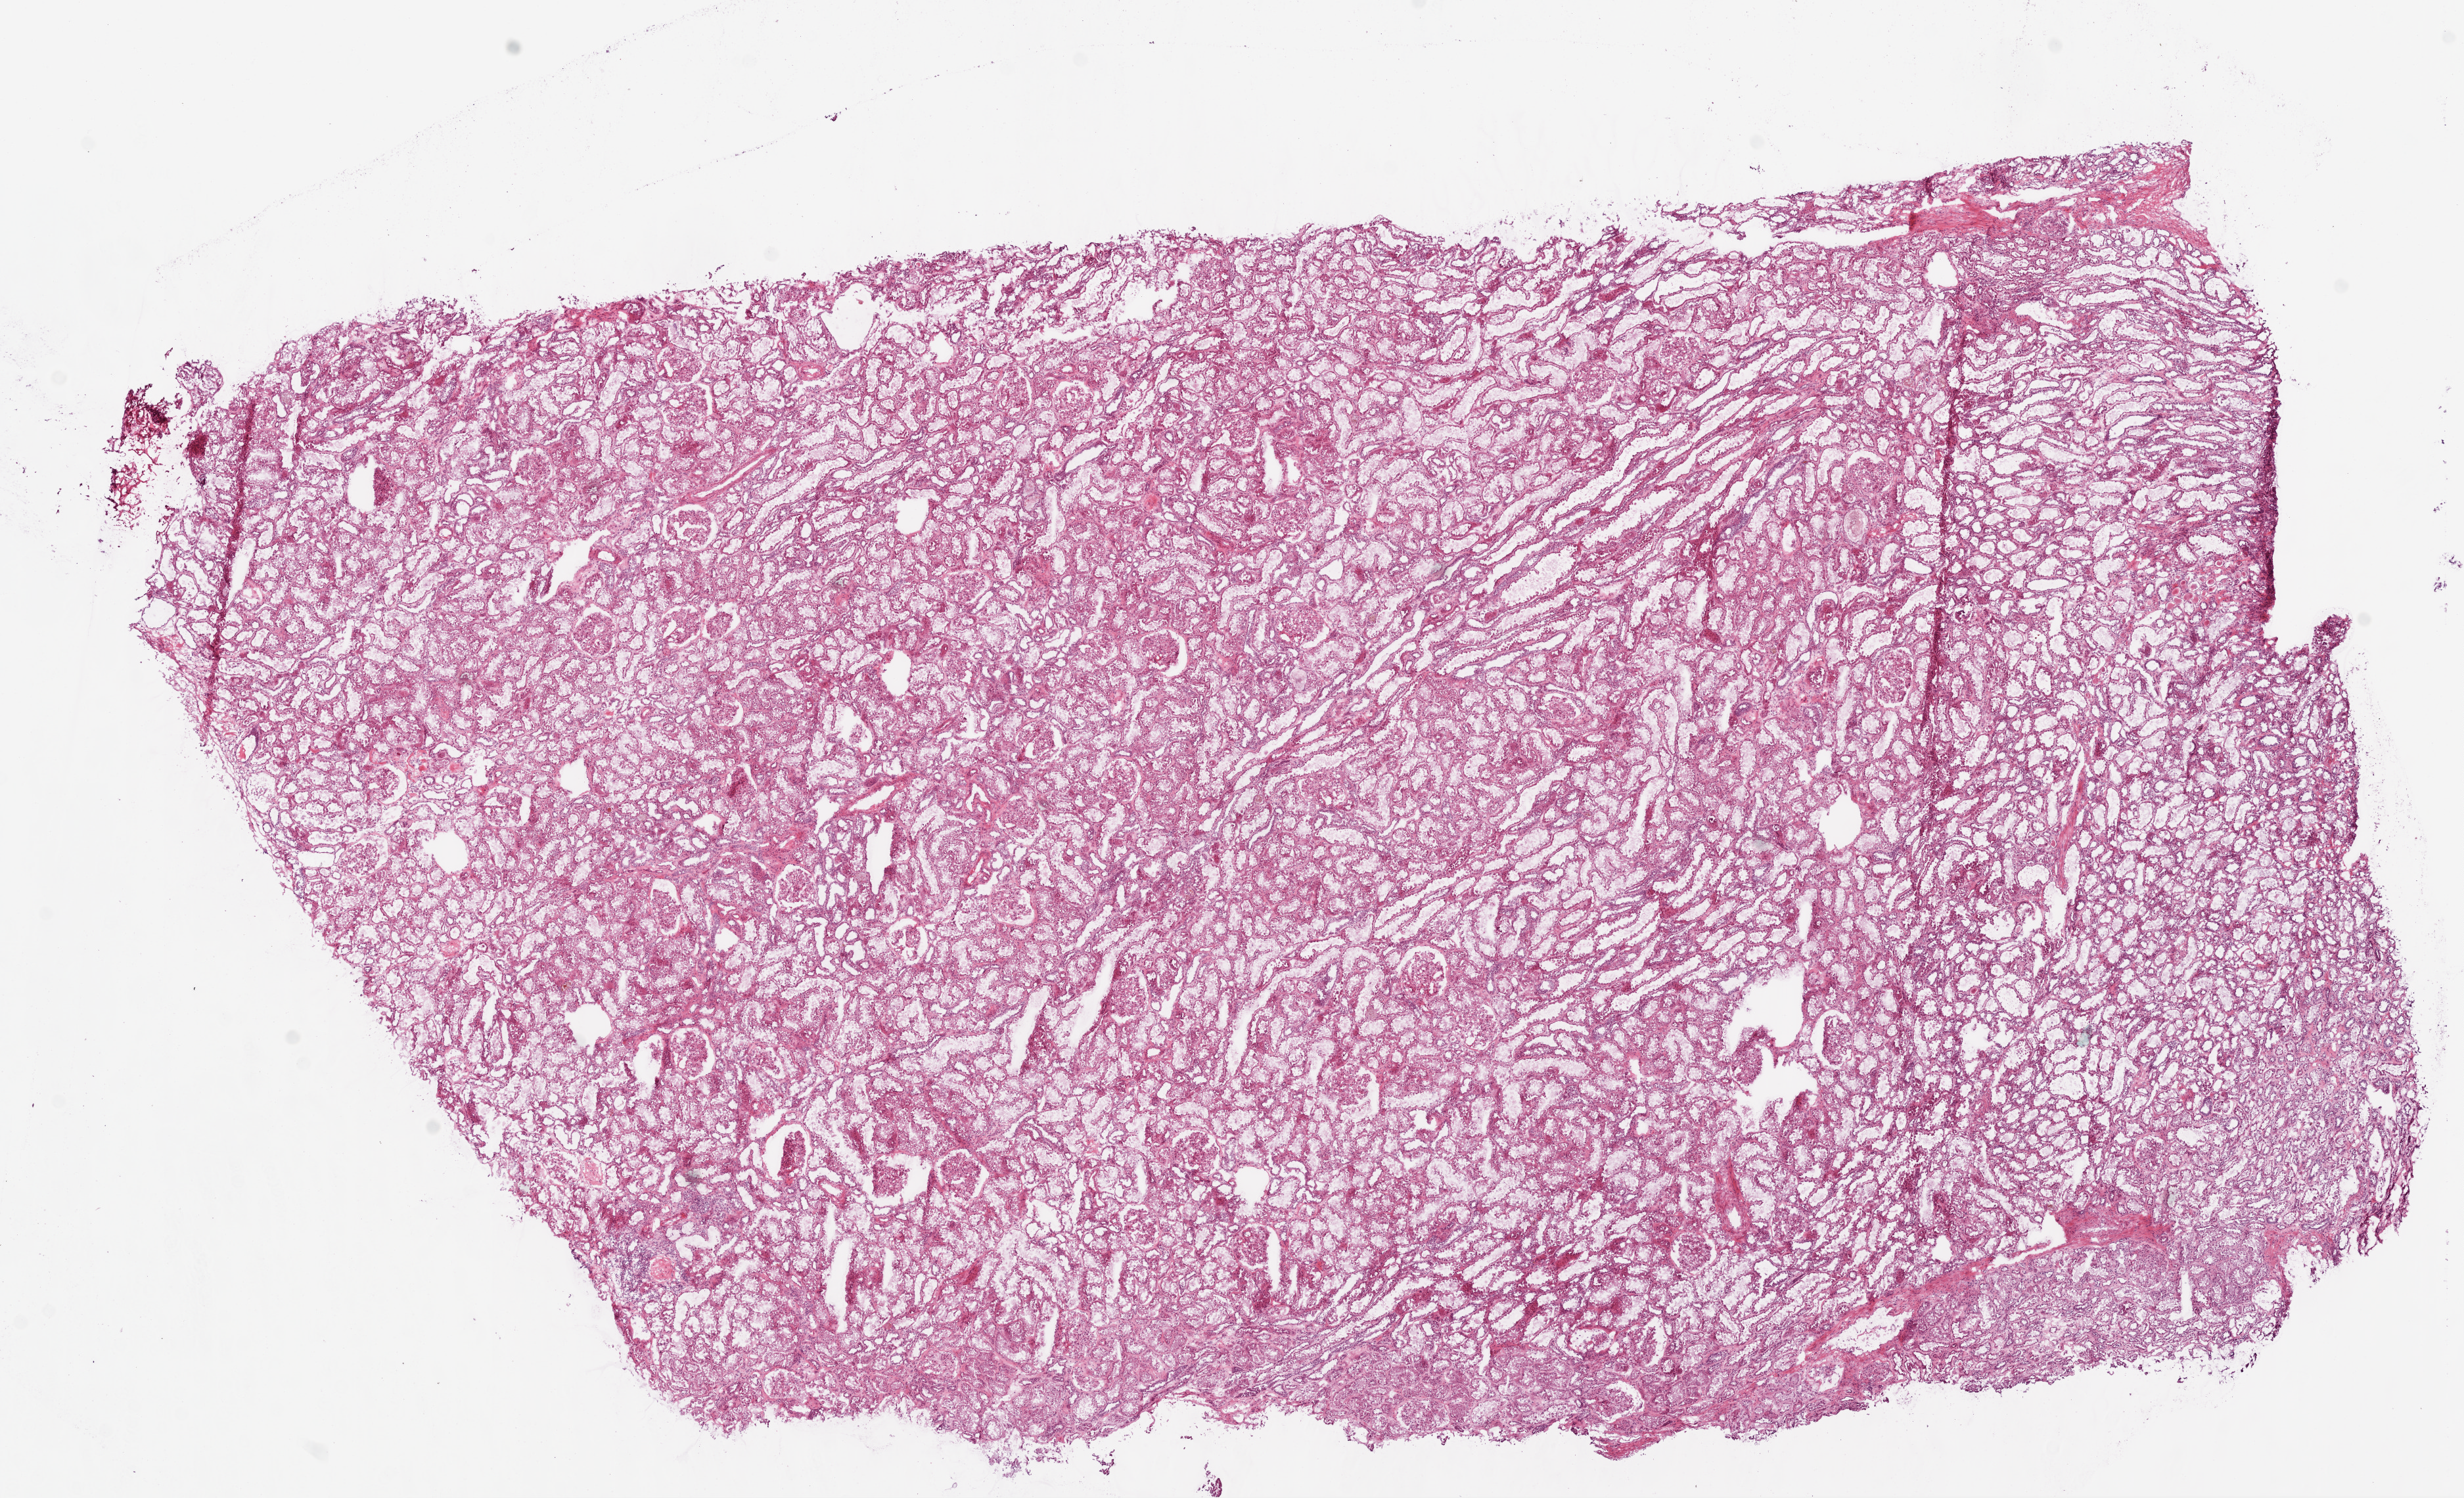
Digitized H&E-stained tissue section (whole slide), low-resolution overview of the scanned area, about 15.0 x 9.1 mm (from a 20x scan). Frozen section from the top of the tissue portion. Kidney, solid tissue normal (non-tumour tissue) sample. Female patient; age at initial diagnosis 53 years.
This section: solid tissue normal (non-tumour) sample from the same patient. Patient diagnosis: Clear cell adenocarcinoma, NOS.